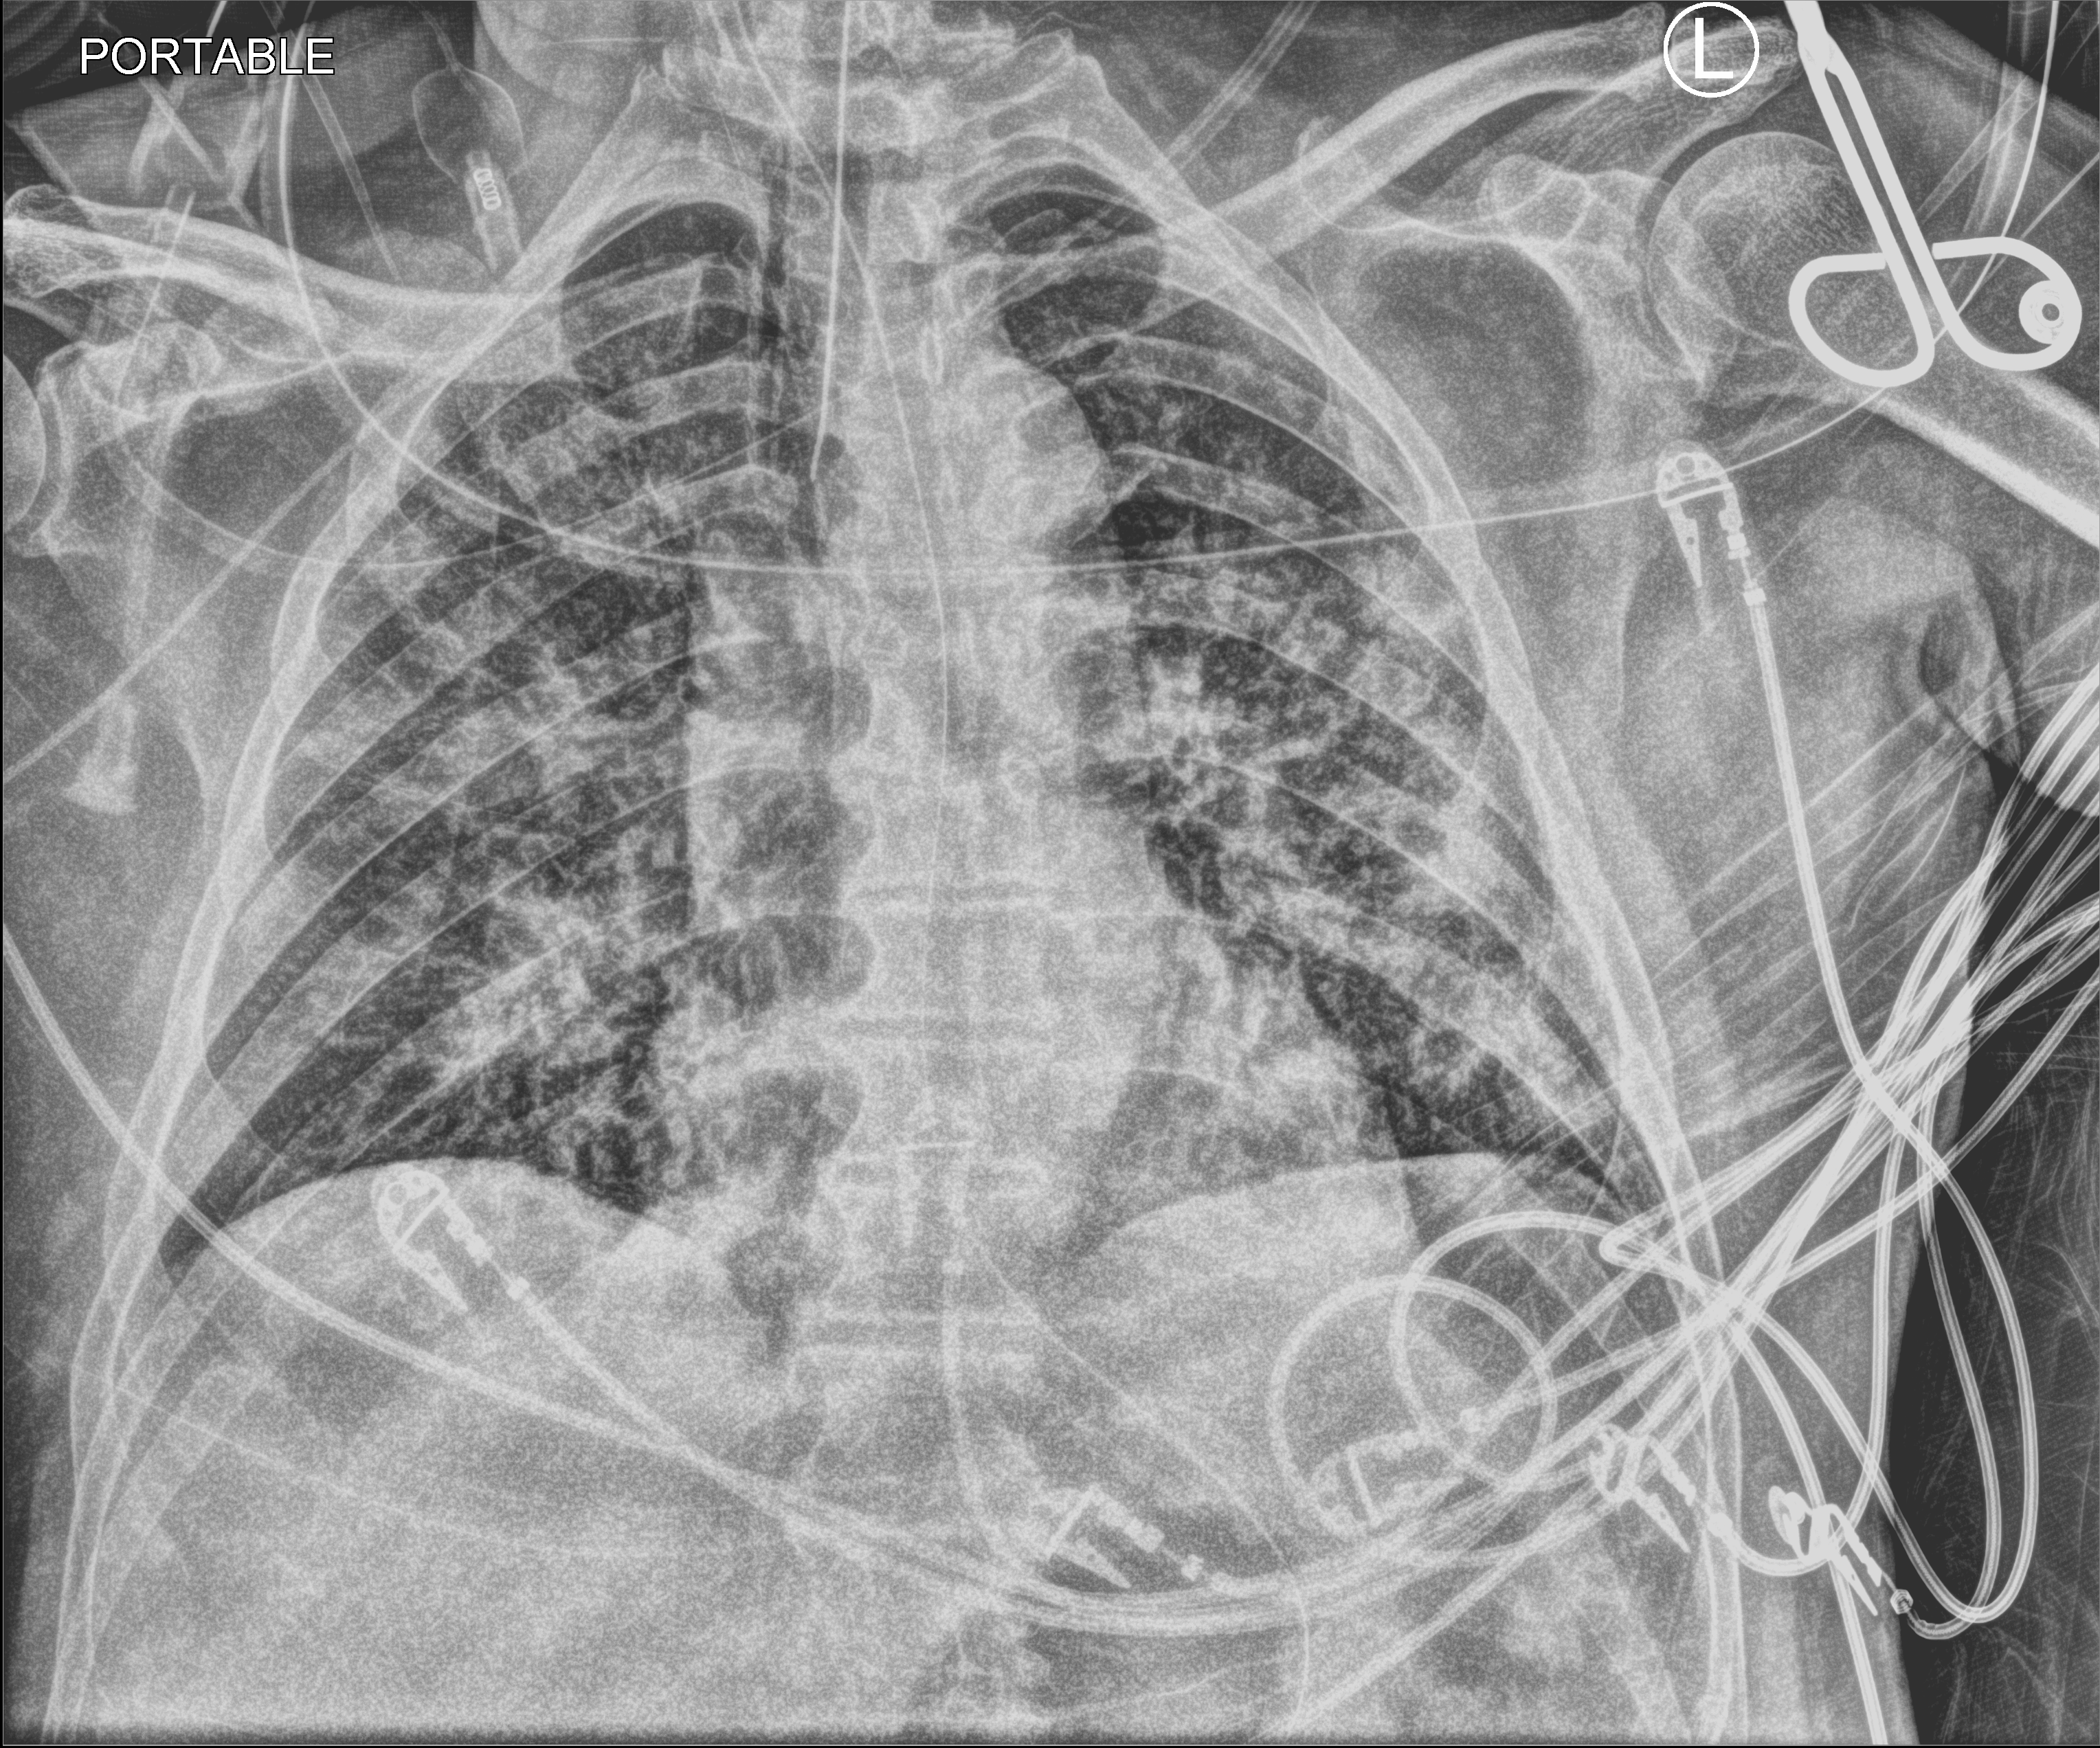
Bedside chest radiograph (computed radiography); anteroposterior (AP) projection. Male patient hospitalised with COVID-19, age 60–74 years.
Hospital-stay facts (about this admission, not read from this image; timing relative to this image not recorded):
- mechanically ventilated during this hospital stay: yes